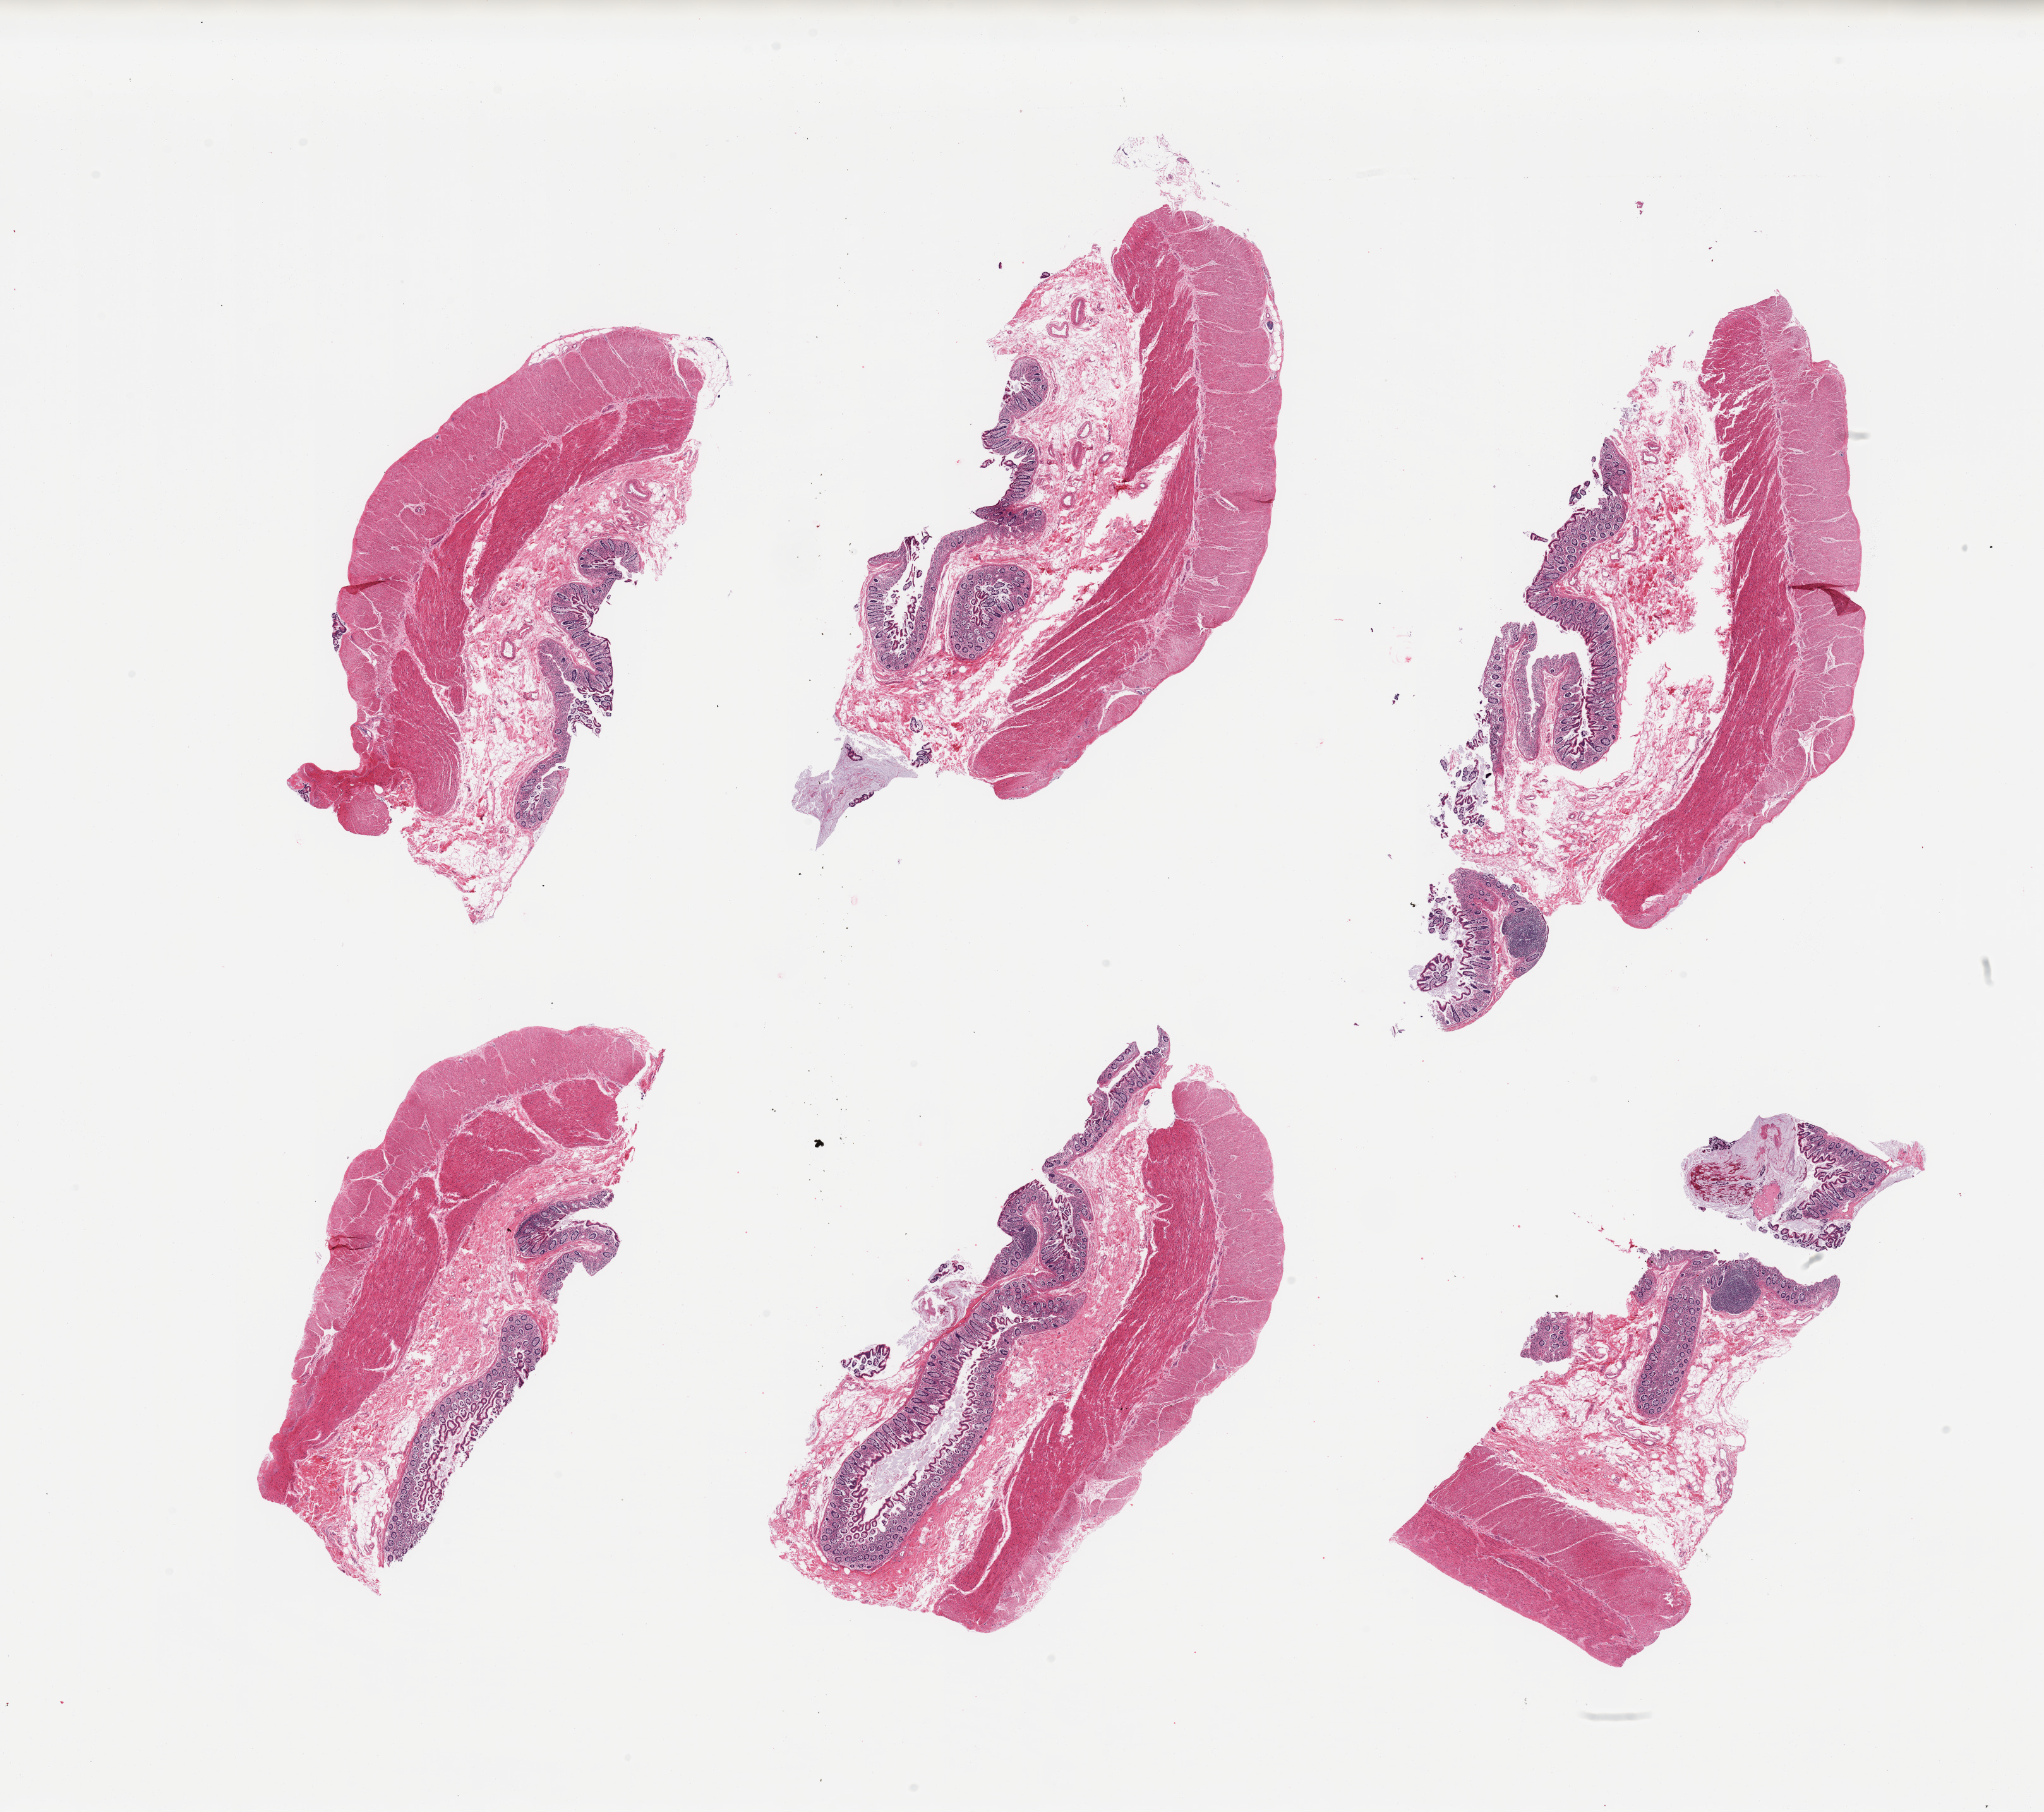
Whole-slide image, haematoxylin and eosin stain — a low-resolution overview of the entire scanned area, about 25.6 x 22.7 mm, PAXgene-fixed, paraffin-embedded tissue, target tissue: transverse colon, tissue donor sample. Male donor.
• review note (as recorded): 6 pieces; full thickness sections, mucosa is moderately autolyzed